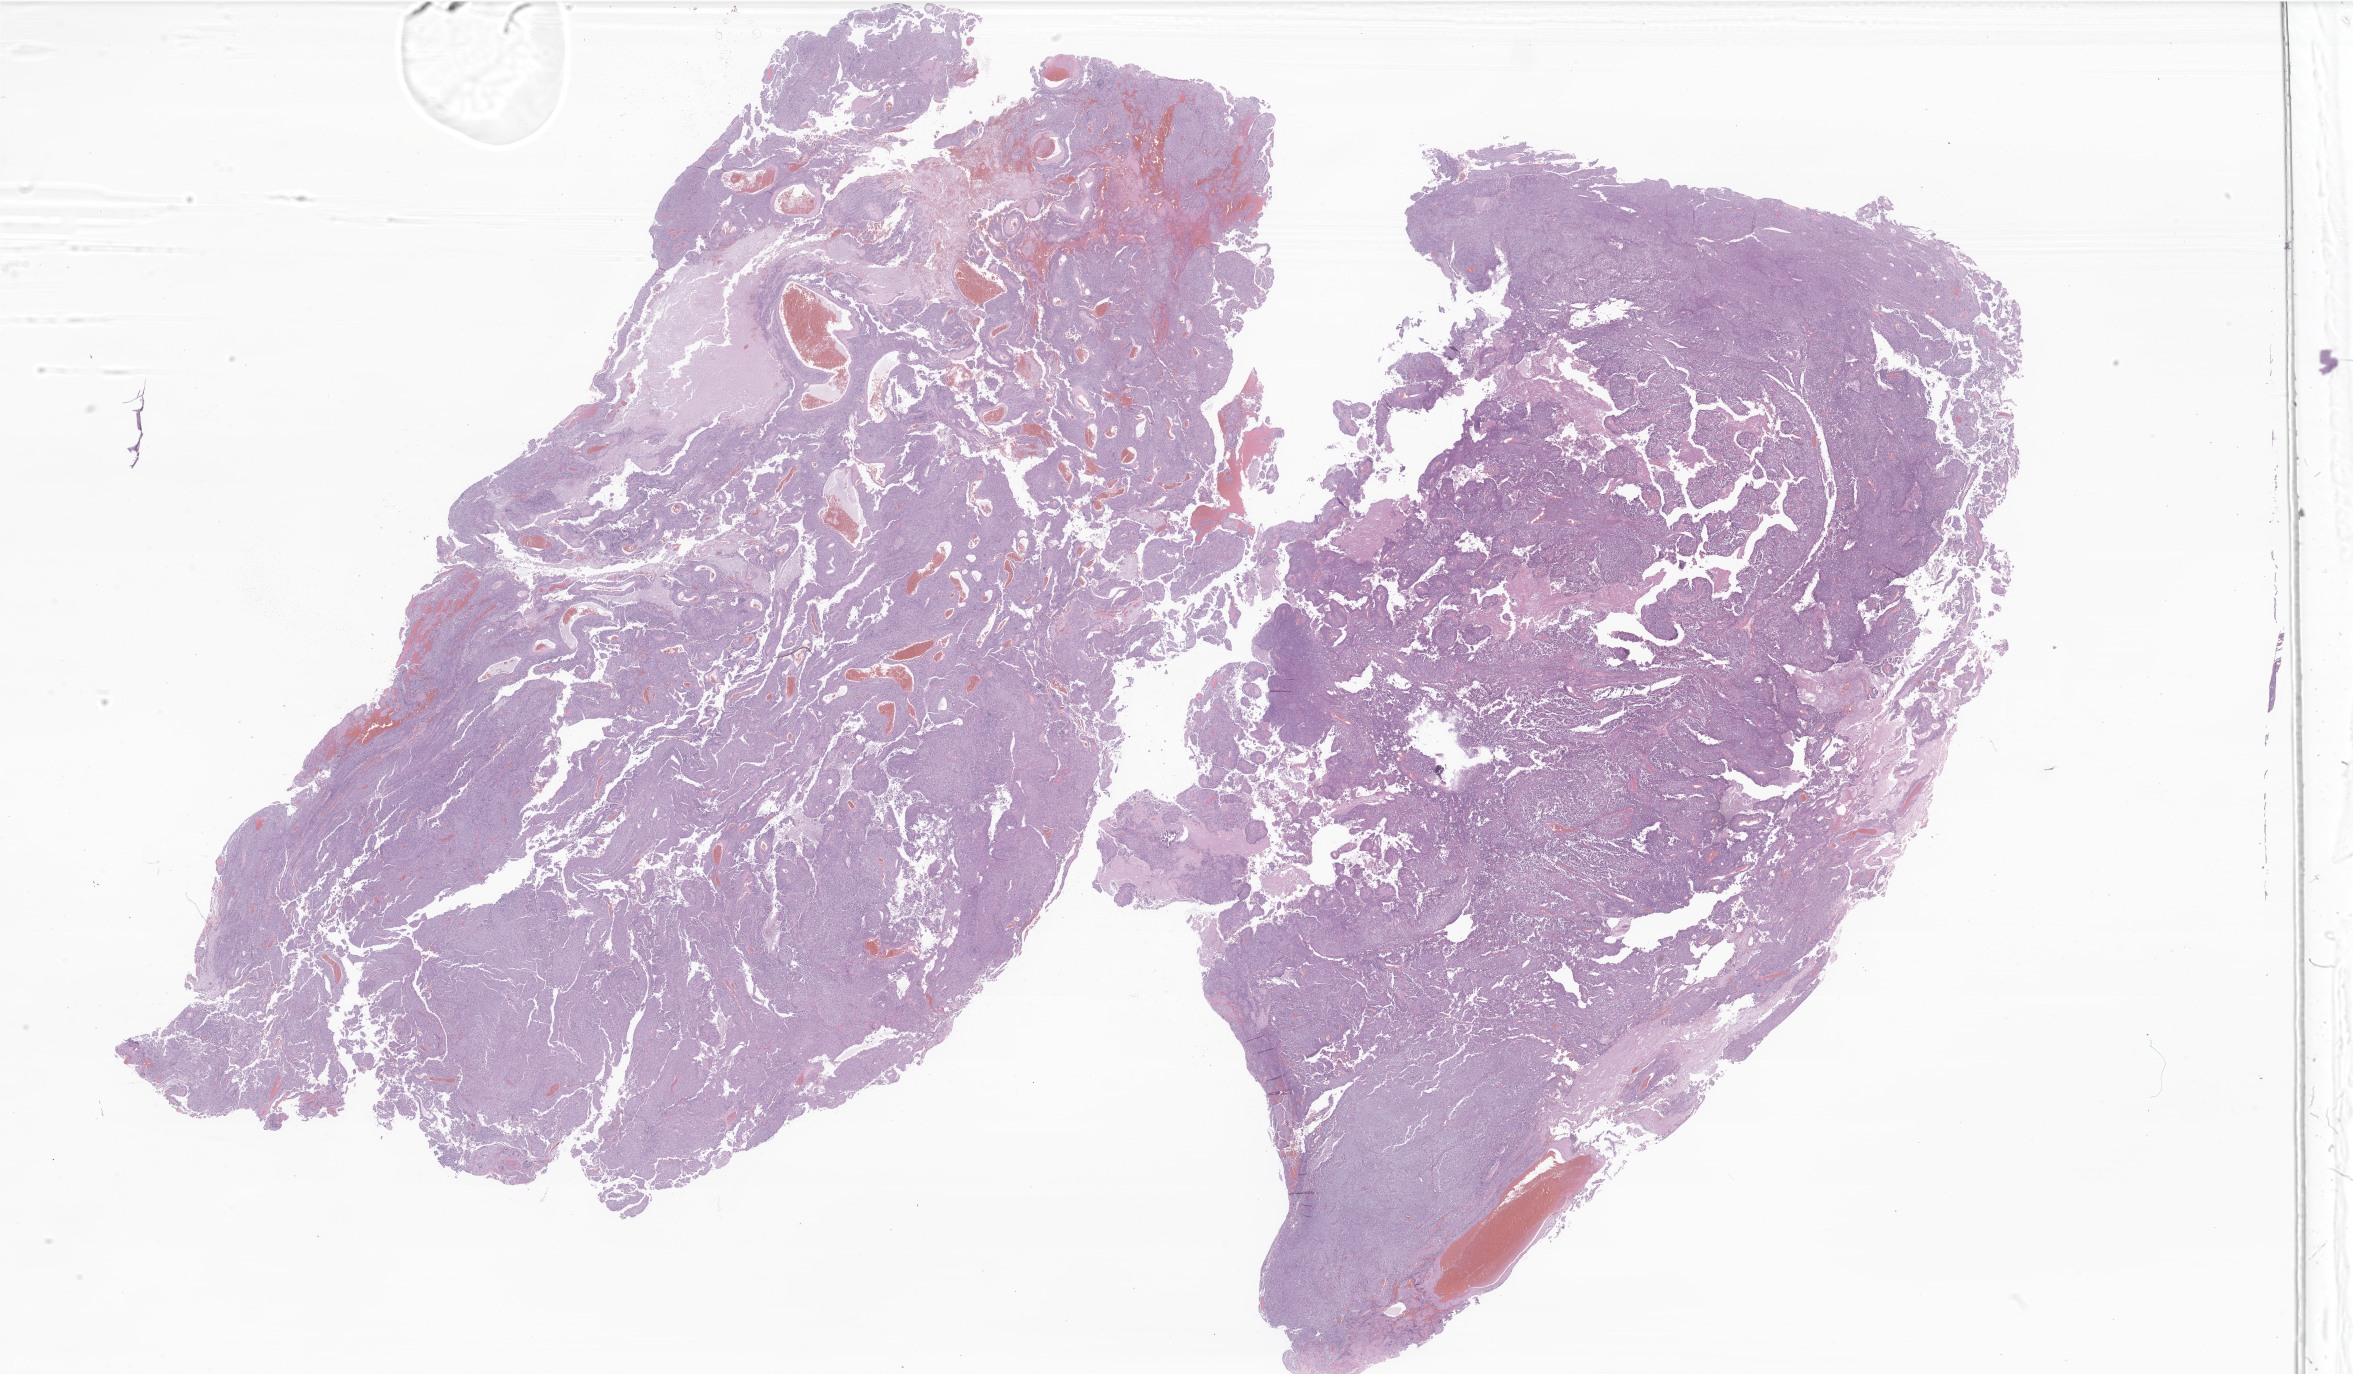
H&E whole-slide image of tumor tissue from the brain — shown as a low-resolution overview of the whole scanned area (about 39.7 x 23.2 mm), FFPE section. Female patient, age 127 months (10 years 7 months).
Recorded diagnosis: Ependymoma, NOS.